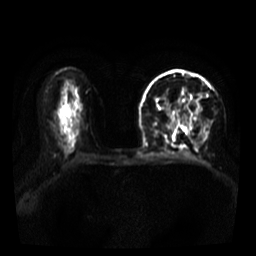
Breast MRI, one axial slice; diffusion-weighted series; image 2 of 4 stored at this slice position (different b-values; order by instance number); 3 T; 5 mm slice thickness; 256 × 256 image matrix, field of view 320 × 320 mm. Female patient.
Outlined on this slice (outlined manually by an expert reader):
- tumour on diffusion-weighted imaging: bounding box (x1, y1, x2, y2) in pixels: (188, 99, 201, 112)